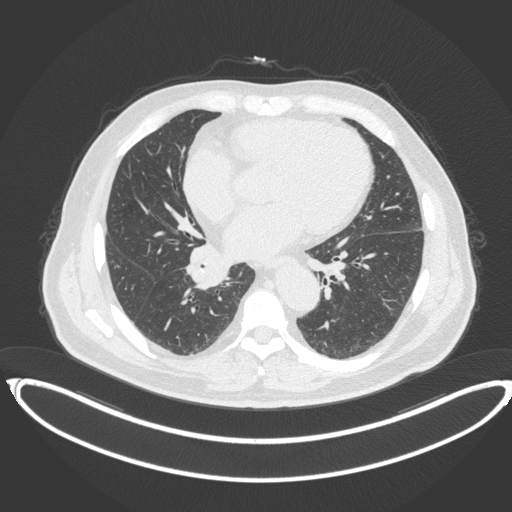
Chest CT, one axial slice. Slice 181 of 383 in the series (ordered by position). Lung window (W 1500 / L -600 HU). 512 × 512 image matrix, field of view 448 × 448 mm. Male patient, age 61 years. From the clinical record (not read from this slice): clinical TNM (as recorded): T1b N1 M0.
Structures marked on this image (bounding box drawn by a radiologist):
- lung tumour (recorded histology: squamous cell carcinoma): bounding box [x1, y1, x2, y2] px = [184, 245, 230, 292]